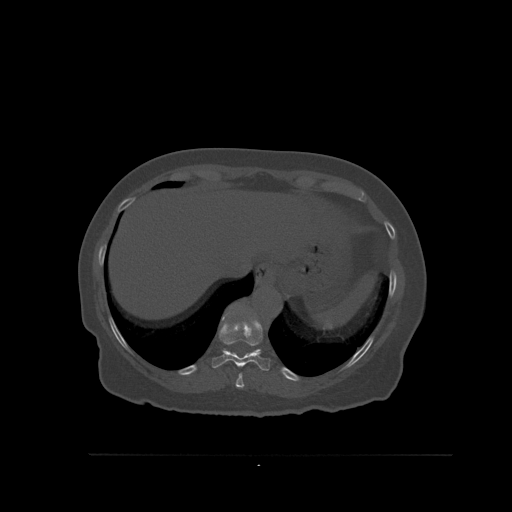
CT including the spine, one axial slice. Slice 319 of 527 in the series (ordered by position). Bone window (W 1800 / L 400 HU). 1.5 mm slice thickness. 512 × 512 image matrix, field of view 470 × 470 mm. Female patient, age 73 years. From the clinical record (not read from this slice): primary cancer: breast; vertebrae with lytic lesions (as recorded): L2.
Annotated regions visible in this slice (semi-automatically segmented with operator editing):
- T10 vertebra: bounding box <211,318,271,371> (left, top, right, bottom; pixels)
- T11 vertebra: <225,303,261,350>
- T9 vertebra: <235,373,244,389>